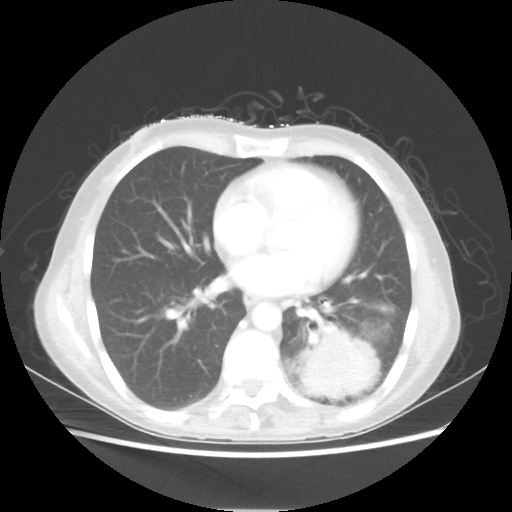
Chest CT, one axial slice; slice 24 of 56 in the series (ordered by position); 80 kVp; lung window (W 1500 / L -600 HU); 5 mm slice thickness; 512 × 512 image matrix, field of view 360 × 360 mm. Patient: female, 53 years. From the clinical record (not read from this slice): clinical TNM (as recorded): T3 N0 M0.
Structures marked on this image (rectangle marked by the reading radiologist):
- lung tumour (recorded histology: adenocarcinoma): box from (x=298, y=327) to (x=380, y=400) px